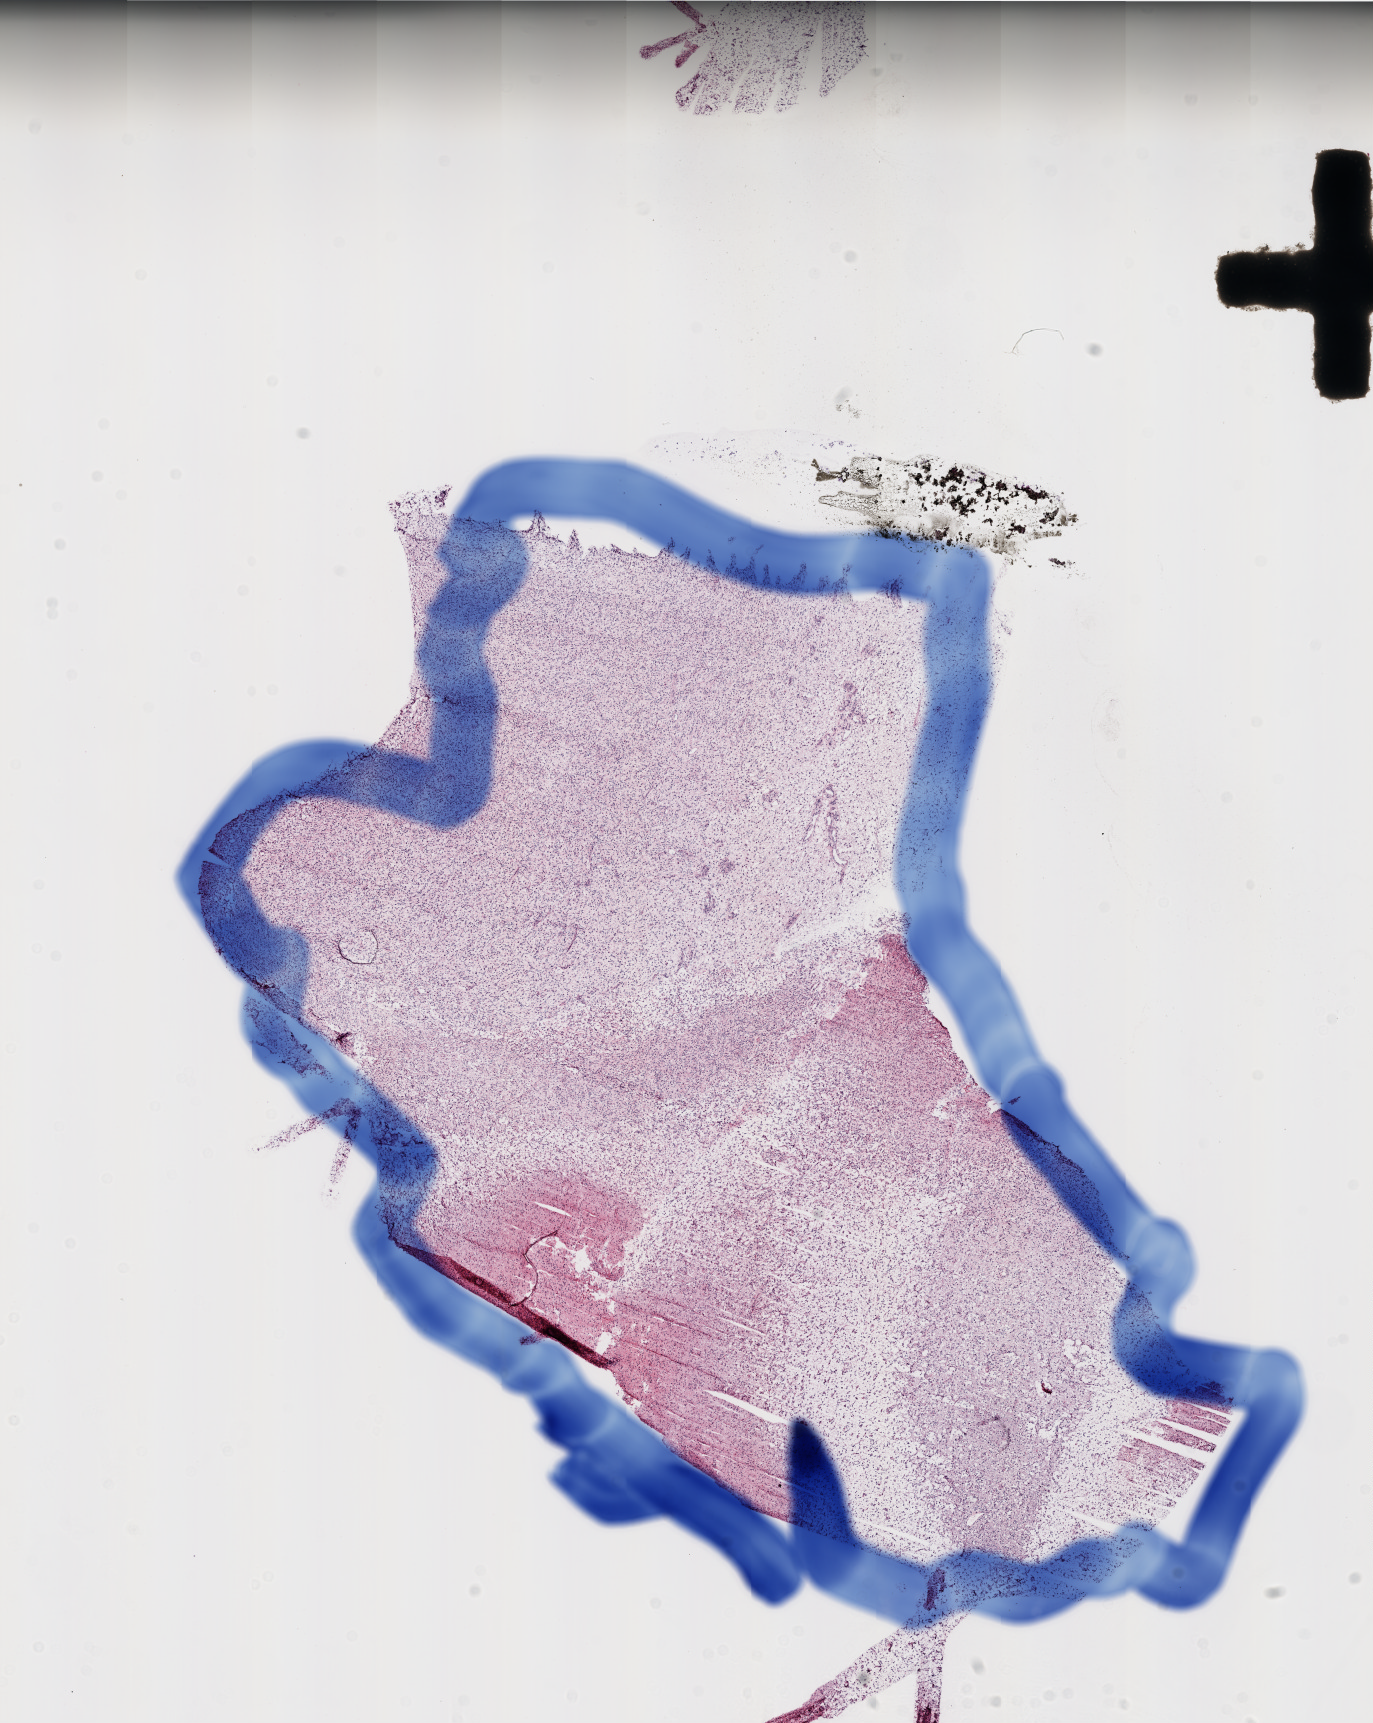
H&E-stained whole-slide image, a low-resolution overview of the entire scanned area, about 11.0 x 13.8 mm (acquisition: 20x scan). Frozen section from the top of the tissue portion. Sample: primary tumour, brain. Male patient; age at initial diagnosis 86 years. Pathologist review of this section (percent, as recorded): tumour cells 95%, tumour nuclei 100%, normal cells 5%, stromal cells 0%, necrosis 0%.
* histologic diagnosis: Glioblastoma